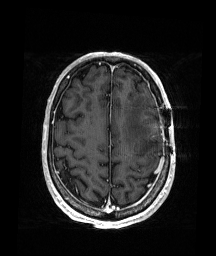
Brain MRI from a brain-tumour surgery series, one axial slice; position 56 of 176 along the scan axis; T1-weighted post-contrast; 216 × 256 image matrix, field of view 219 × 260 mm. Case-level facts recorded for this patient, not image findings: histopathology: Glioblastoma; WHO grade: 4; IDH mutation: no; tumour location: Left Frontal.
Annotated regions visible in this slice (expert manual segmentation):
- tumour: bounding box <147,123,159,133> (left, top, right, bottom; pixels)